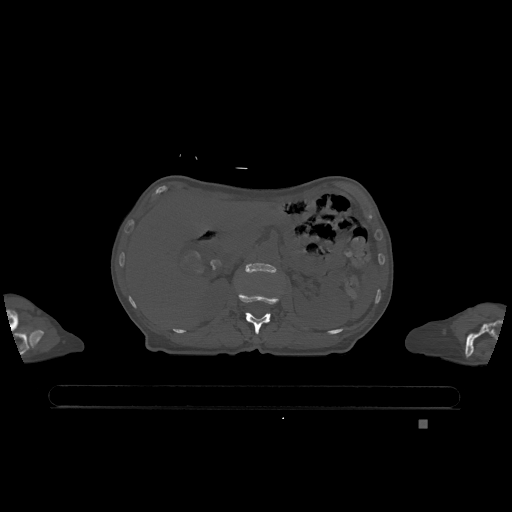
CT including the spine, one axial slice. Slice 463 of 1317 in the series (ordered by position). Bone window (W 1800 / L 400 HU). 0.5 mm slice thickness. 512 × 512 image matrix, field of view 500 × 500 mm. Female patient, age 74 years. Case-level facts recorded for this patient, not image findings: primary cancer: lung; vertebrae with lytic lesions (as recorded): T1, T4, T5, T6, L4, L5.
Structures marked on this image (semi-automatic segmentation, software-assisted and operator-edited):
- L1 vertebra: bounding box <238,292,279,334> (left, top, right, bottom; pixels)
- L2 vertebra: <246,263,276,273>